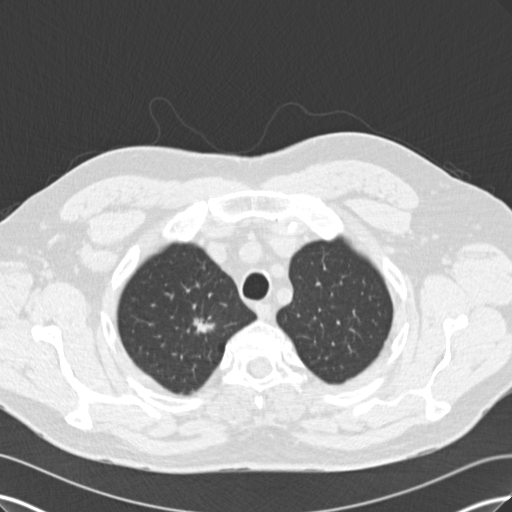
Axial slice from a low-dose chest CT screening exam; baseline annual screen; lung window (W 1500 / L -600 HU); 2 mm slice thickness; 120 kVp; slice 24 of 171 in the series. Male participant, aged 56 years at enrolment. Former smoker at enrolment.
• Expert-annotated lung lesion, bounding box (x1, y1, x2, y2) in pixels: (174, 307, 226, 351).
• The exam's reader record, not a measurement of the box and not confirmed to be the same lesion: non-calcified nodule or mass ≥4 mm, right upper lobe, 14 × 8 mm, spiculated (stellate) margins.
• Later outcome: lung cancer diagnosed 146 days after this screen — adenocarcinoma, NOS, right upper lobe, poorly differentiated (G3), stage IA (AJCC 6th edition), 12 mm at pathology.